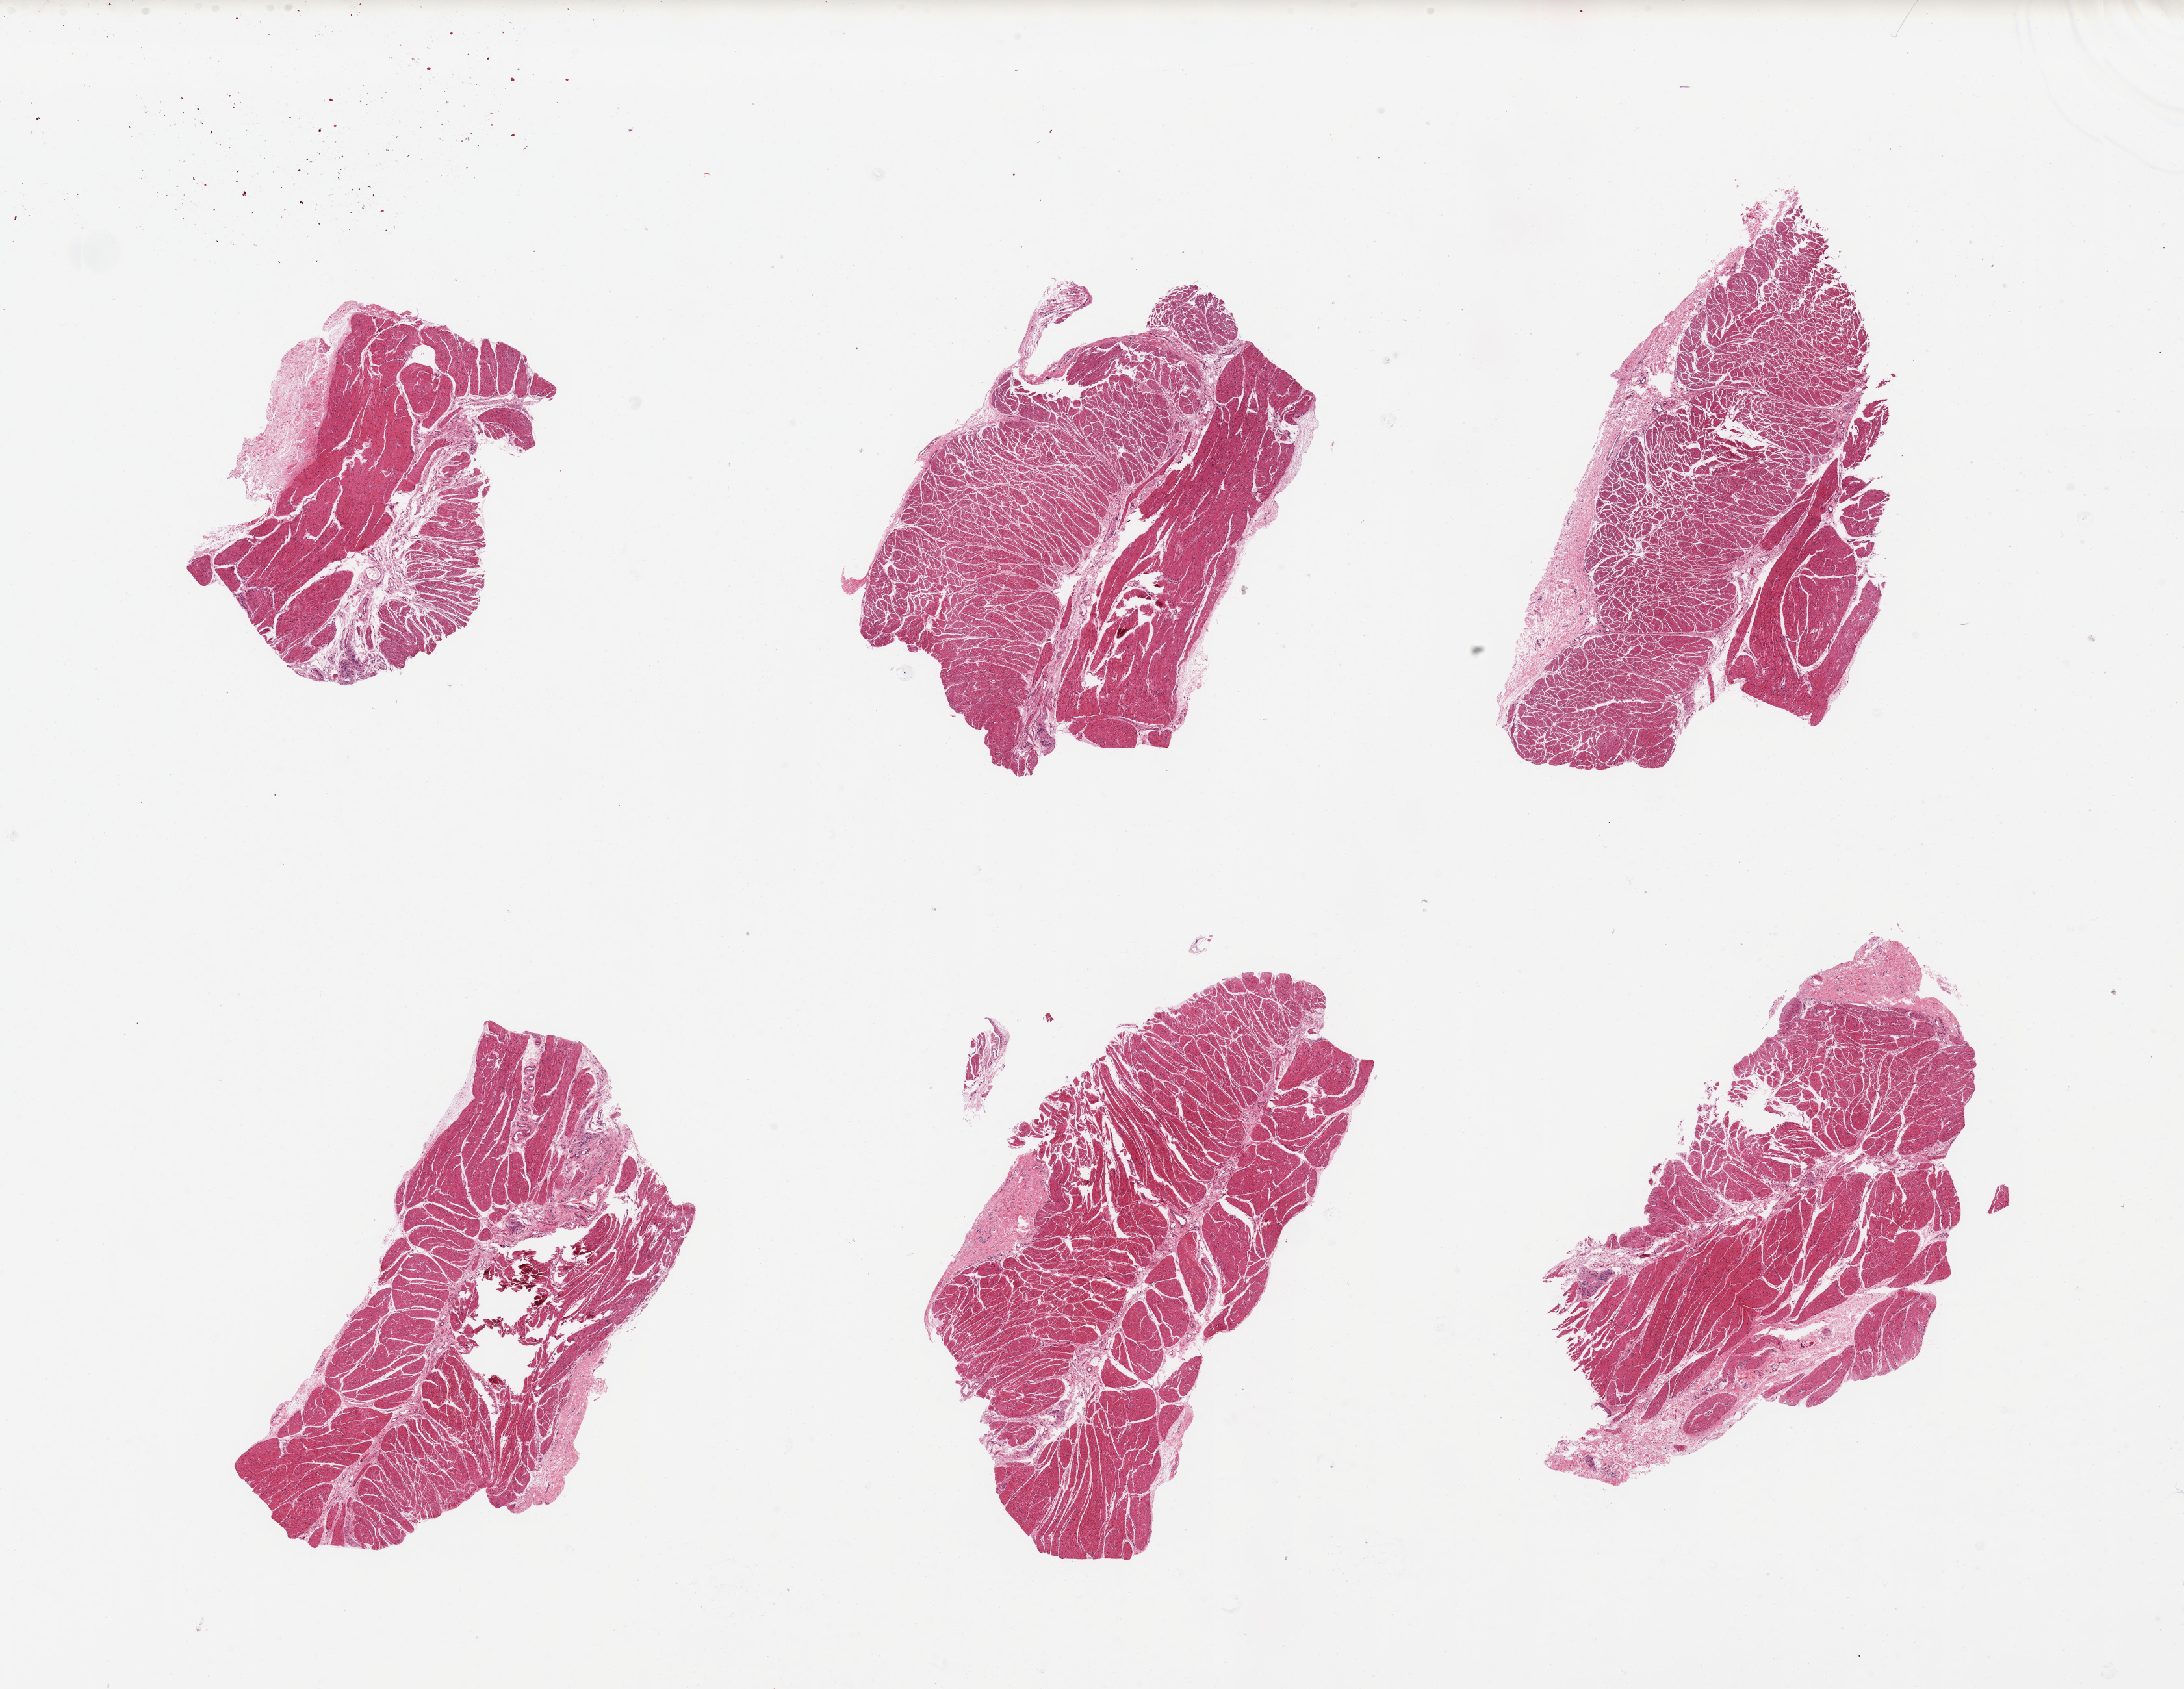
Digitized H&E-stained section — shown as a low-resolution overview of the whole scanned area (about 26.6 x 20.6 mm, acquisition: 20x scan). PAXgene-fixed, paraffin-embedded tissue. Section of esophageal muscle (target tissue). Donor tissue sample. Donor sex: male.
Review note (as recorded): 6 pieces; target muscularis.